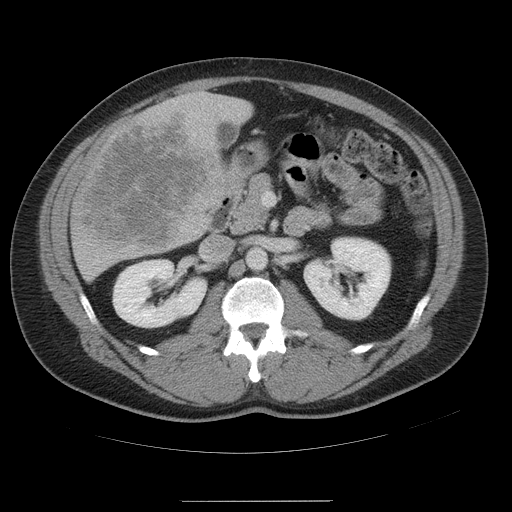
Contrast-enhanced abdominal CT, one axial slice. Position 23 of 54 along the scan axis. 120 kVp. Intravenous contrast given. Soft-tissue window (W 400 / L 40 HU). 5 mm slice thickness. 512 × 512 image matrix. Male patient, age 40 years. Case-level facts recorded for this patient, not image findings: diagnosis: colorectal cancer liver metastases, imaged before liver resection; multiple liver metastases: no; largest metastasis: 15 cm; disease in both lobes: no.
Structures marked on this image (expert manual segmentation):
- liver: bounding box <70,92,251,282> (left, top, right, bottom; pixels)
- planned liver remnant (the part of the liver to remain after resection): <229,98,251,124>
- liver metastasis: <72,107,219,254>